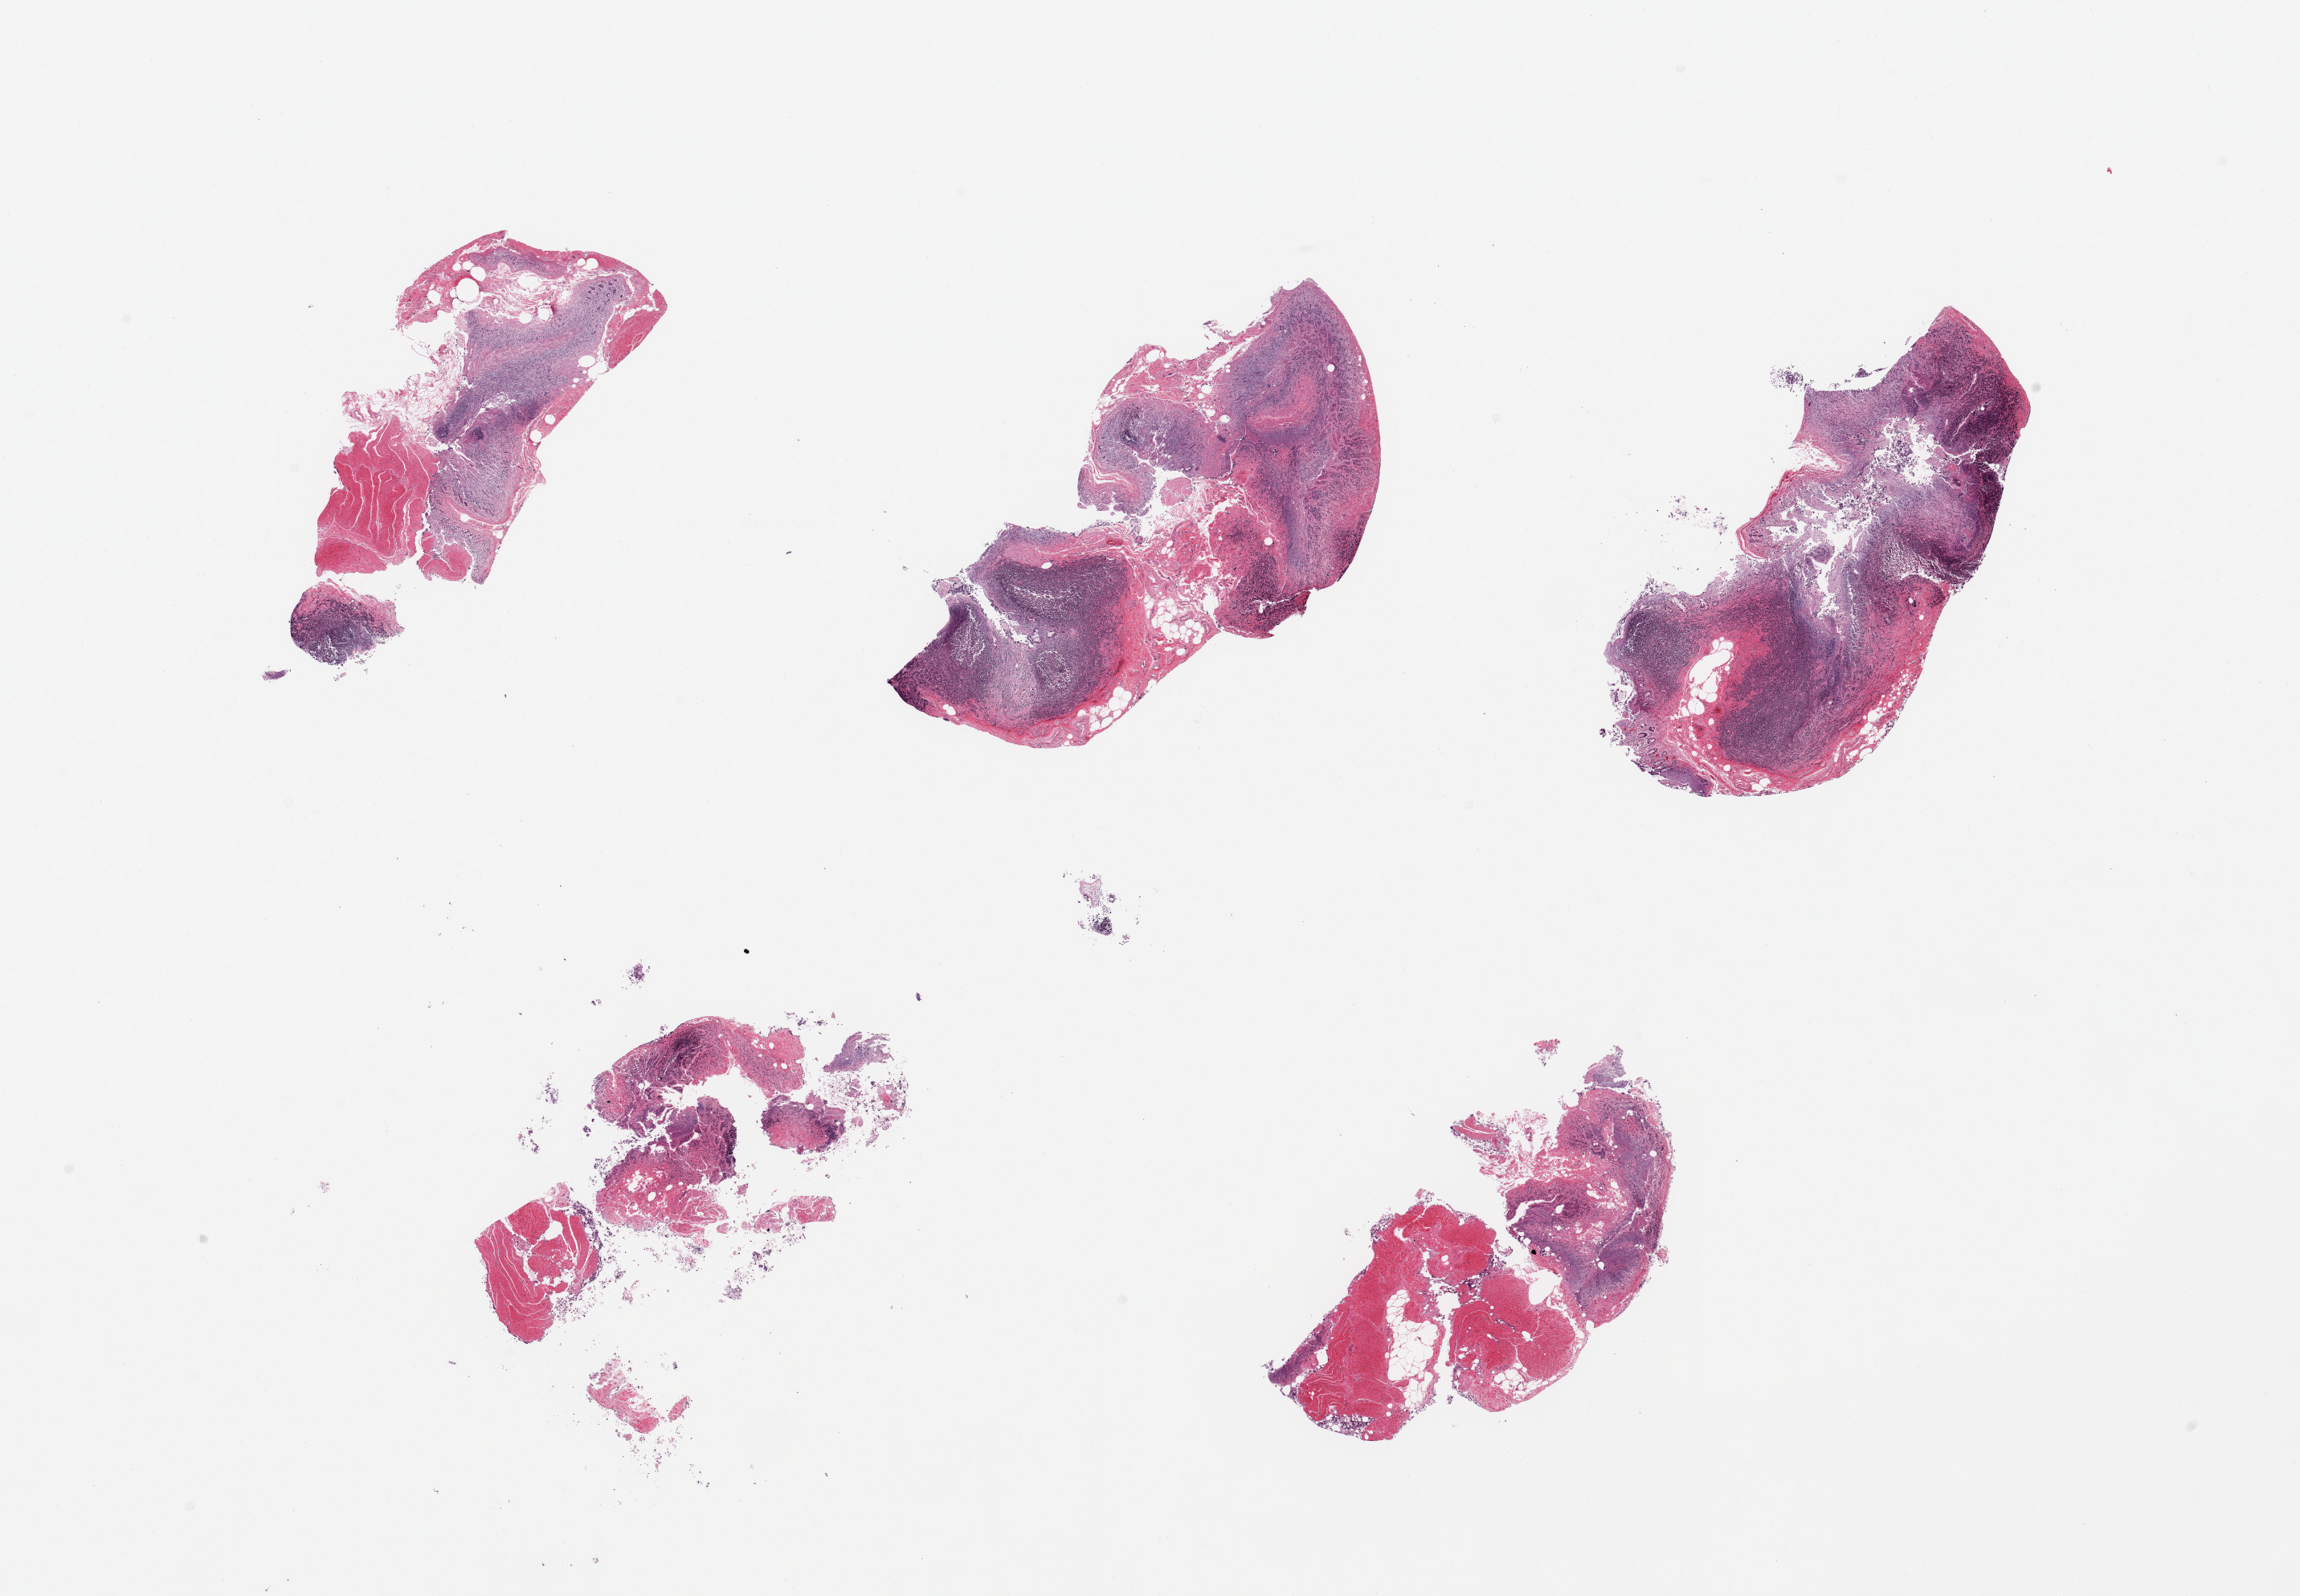
Haematoxylin and eosin whole-slide image — a low-resolution overview of the entire scanned area, about 22.6 x 15.7 mm, PAXgene-fixed paraffin-embedded (PFPE) section, target tissue: ileum, tissue donor sample. Donor sex: male.
• reviewer comment on this tissue sample: 5 pieces, glandular elements with advanced autolysis; ~30% residual target lymphoid elements